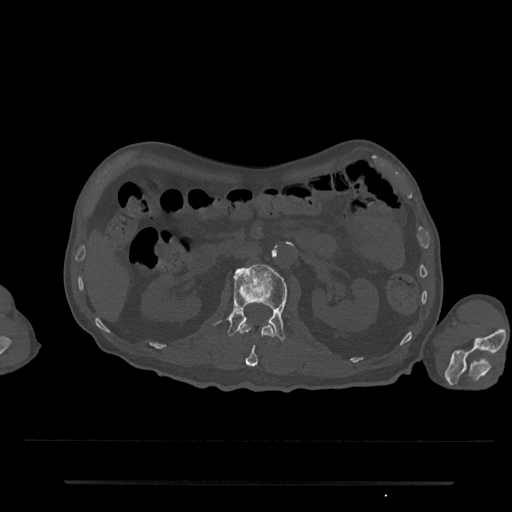
CT including the spine, one axial slice. Position 87 of 797 along the scan axis. Reconstruction kernel Br40s/3. 120 kVp. Bone window (W 1800 / L 400 HU). 512 × 512 image matrix, field of view 427 × 427 mm. Male patient, age 74 years. Case-level facts recorded for this patient, not image findings: primary cancer: prostate.
Structures marked on this image (semi-automatically segmented with operator editing):
- L1 vertebra: bounding box <239,322,274,367> (left, top, right, bottom; pixels)
- L2 vertebra: <227,264,288,341>